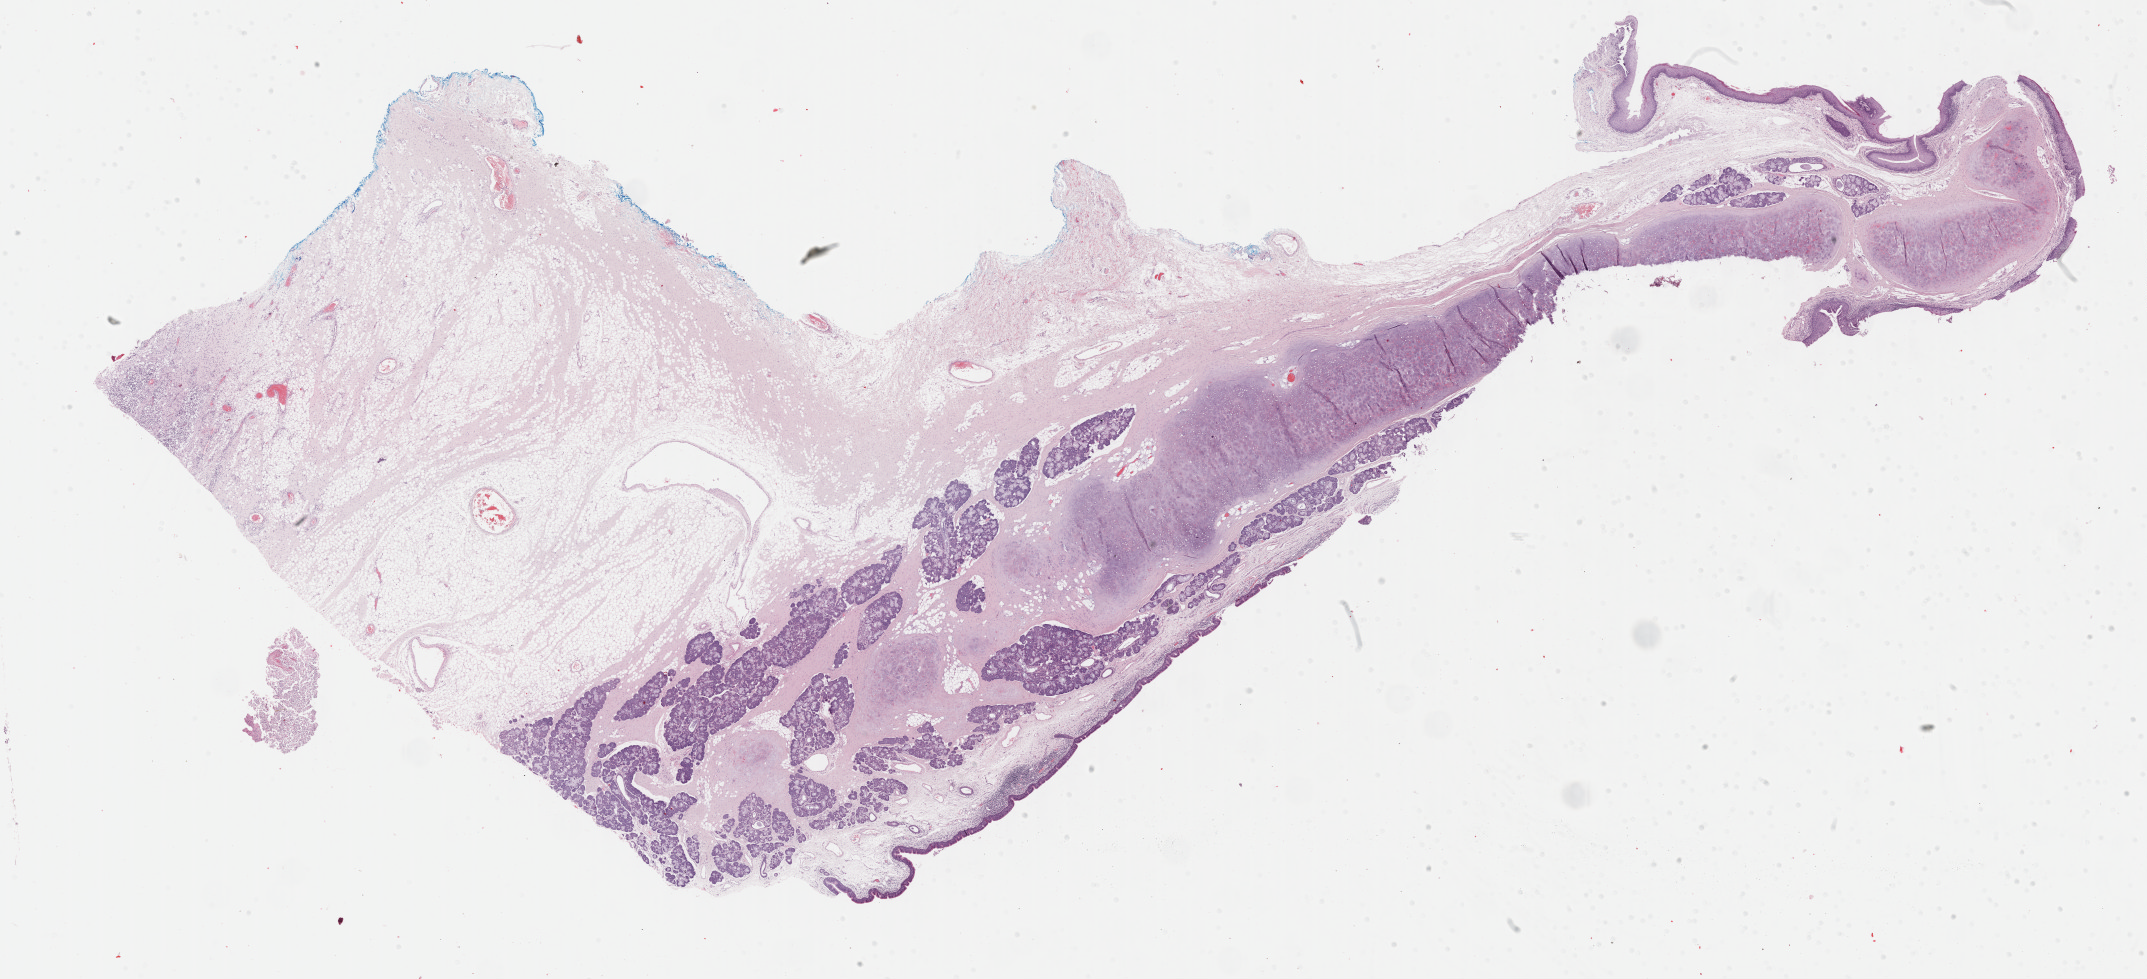
Whole-slide histology image, Hematoxylin and eosin (H&E) stained — shown as a low-resolution overview of the whole scanned area (about 34.7 x 15.8 mm). Formalin-fixed paraffin-embedded (FFPE) diagnostic section. Primary tumour sample from the head and neck. Male patient; age at initial diagnosis 50 years. Histologic grade: G2 (moderately differentiated).
TNM: T4a N0 M0. AJCC pathologic stage: IVA (7th edition). Pathologic diagnosis: Squamous cell carcinoma, NOS (larynx, NOS). Laterality: left.